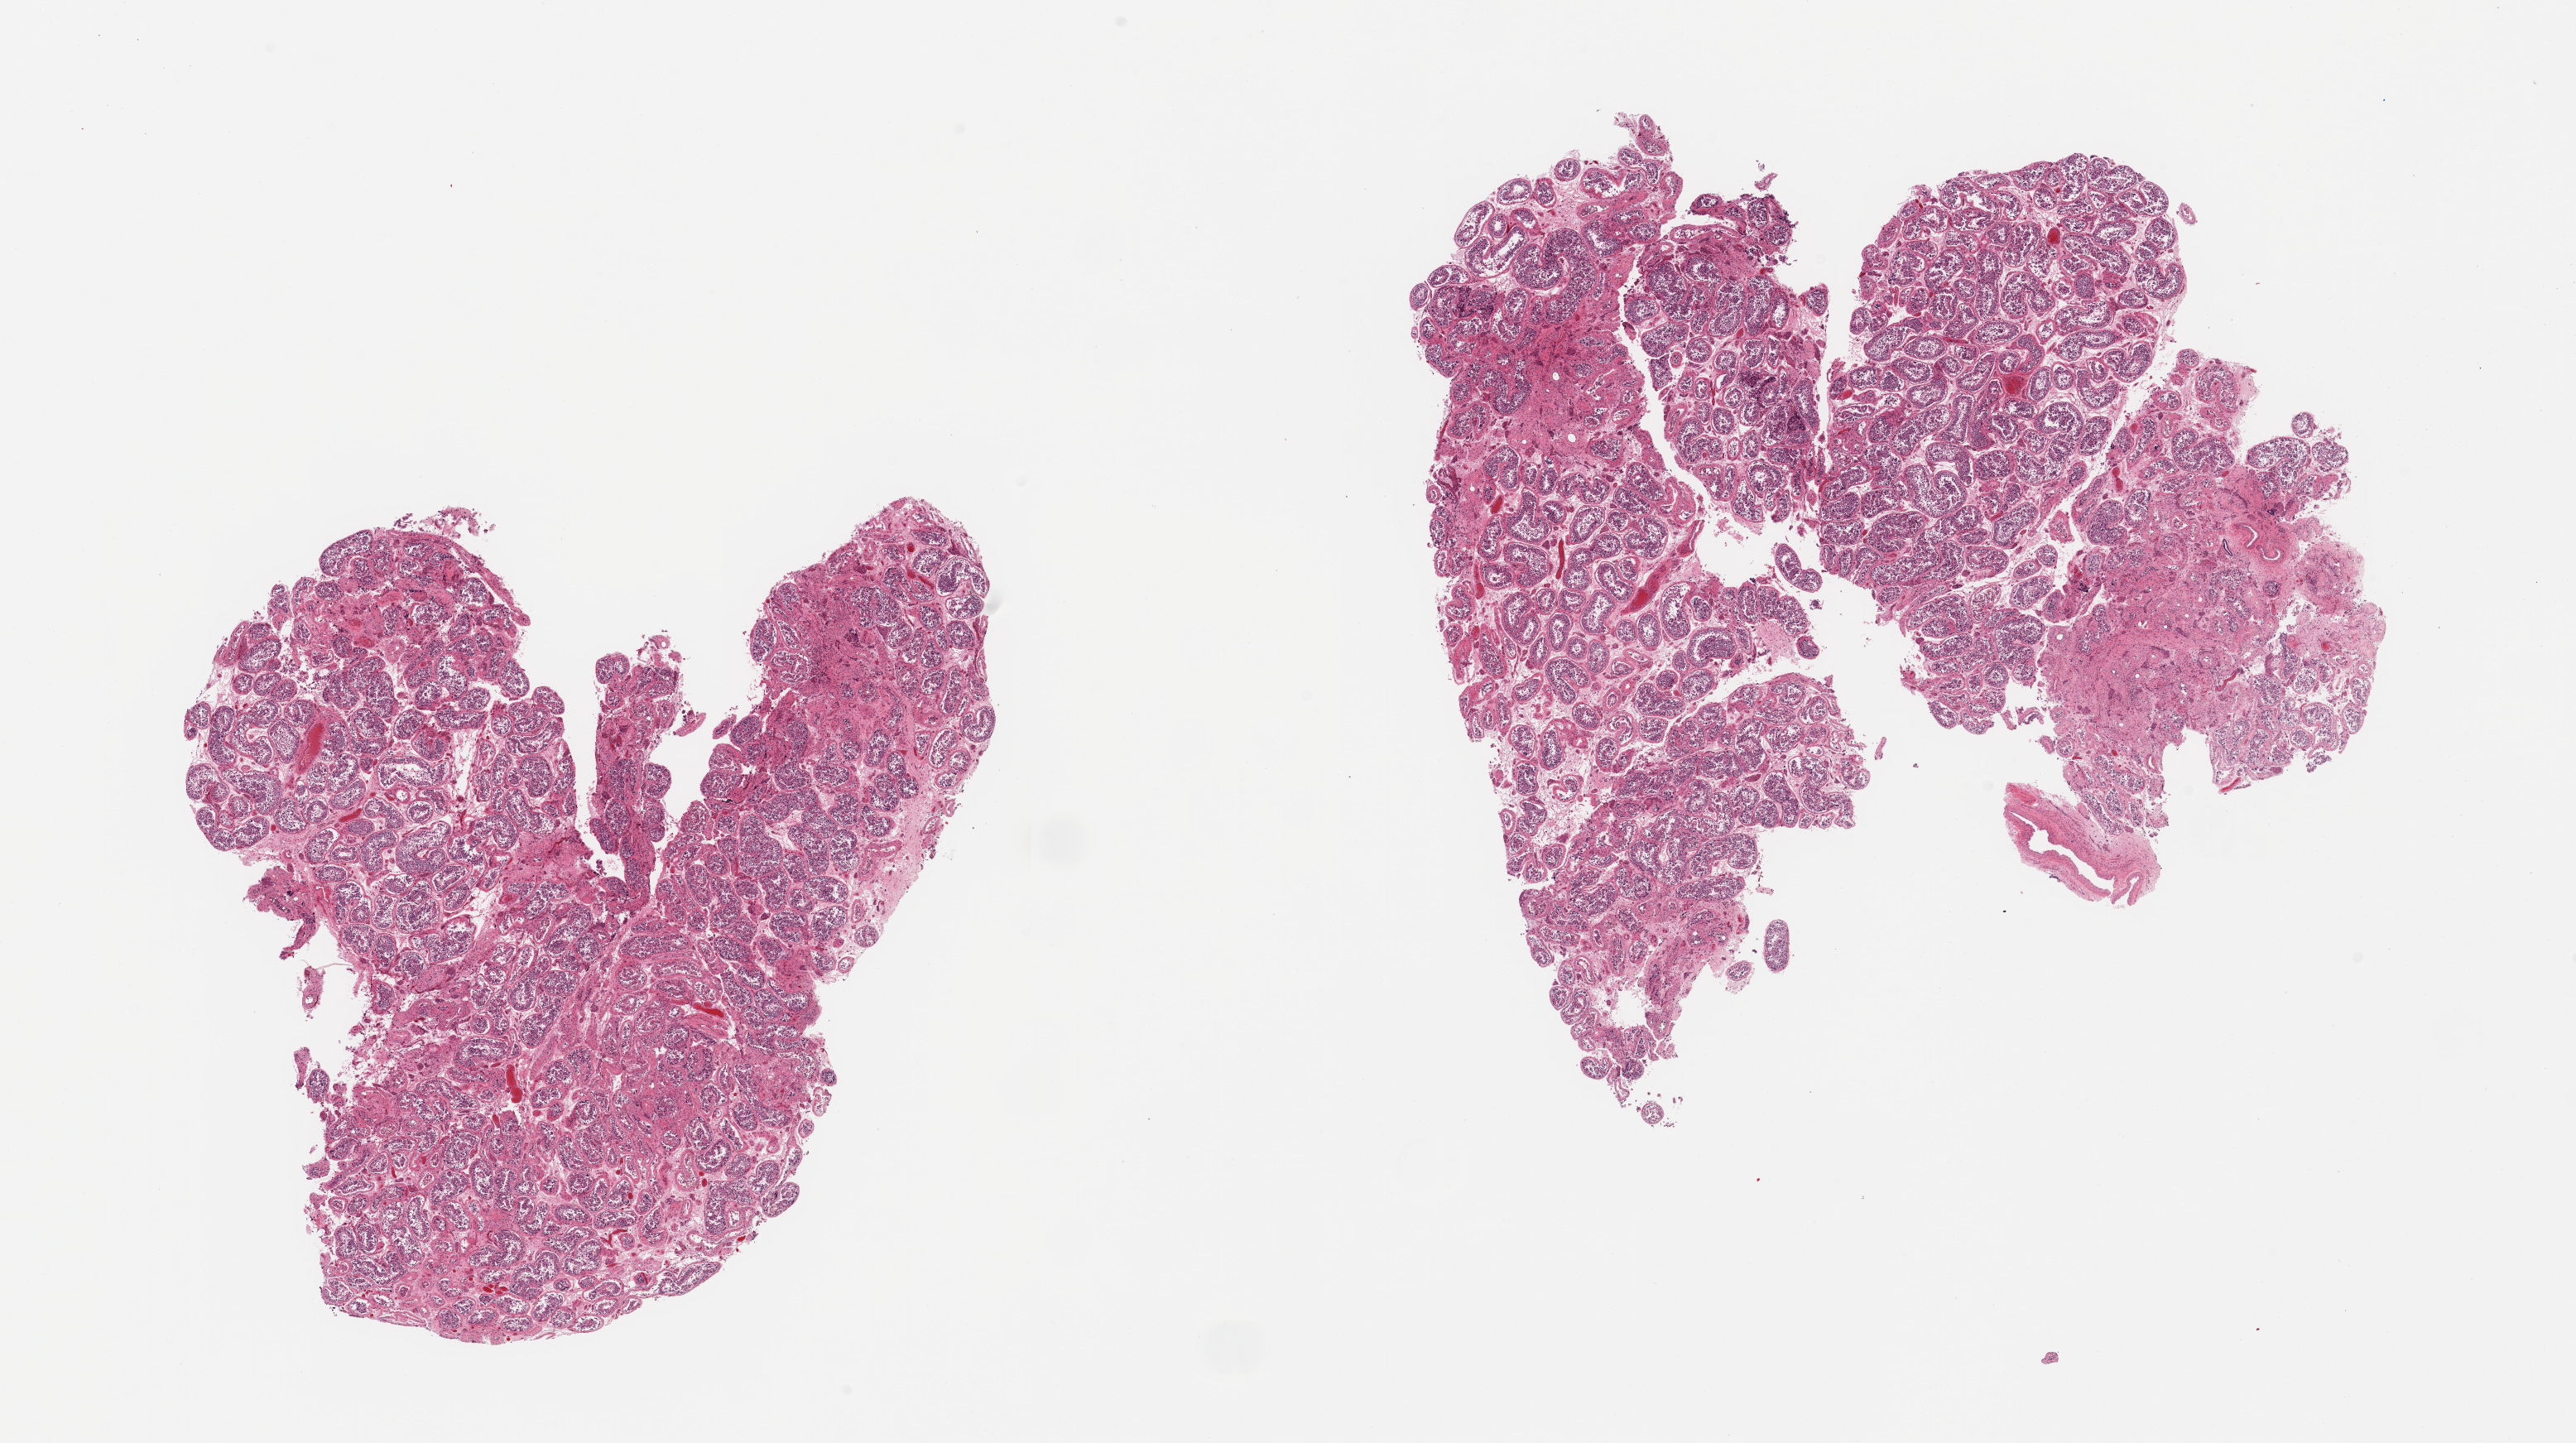
Whole-slide image, hematoxylin and eosin (H&E) stain — shown as a low-resolution overview of the whole scanned area (about 24.6 x 13.8 mm, from a 20x scan). PAXgene-fixed, paraffin-embedded tissue. Sampled site (target tissue): testis. Tissue donor sample. Donor sex: male.
Review note (as recorded): 2 pieces; spermatogenesis; several foci, up to 2 mm of fibrosis and Leydig cell hyperplasia.